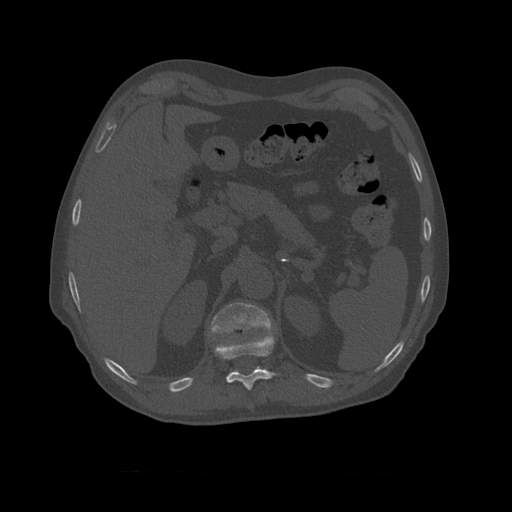
CT including the spine, one axial slice; slice 396 of 450 in the series (ordered by position); reconstruction kernel STANDARD; bone window (W 1800 / L 400 HU); 512 × 512 image matrix, field of view 405 × 405 mm. Patient age 75 years. From the clinical record (not read from this slice): primary cancer: prostate.
Structures marked on this image (semi-automatic segmentation, software-assisted and operator-edited):
- T10 vertebra: bounding box [x1, y1, x2, y2] px = [214, 333, 277, 391]
- T11 vertebra: [209, 303, 273, 354]